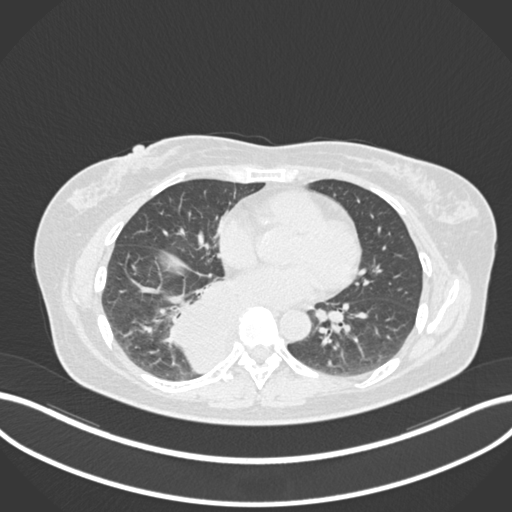
Chest CT, one axial slice; slice 571 of 677 in the series (ordered by position); reconstruction kernel B30f; 120 kVp; lung window (W 1500 / L -600 HU); 512 × 512 image matrix. Patient: female, 54 years. Case-level facts recorded for this patient, not image findings: clinical TNM (as recorded): T4 N0 M0.
Structures marked on this image (bounding box drawn by a radiologist):
- lung tumour (recorded histology: adenocarcinoma): box from (x=159, y=278) to (x=238, y=375) px